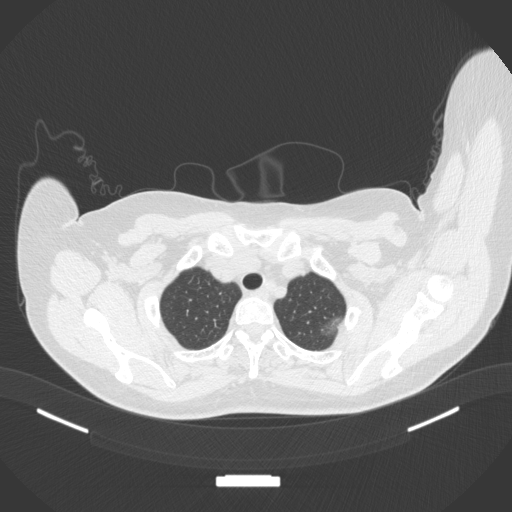
Chest CT, one axial slice; position 325 of 386 along the scan axis; reconstruction kernel B31f; lung window (W 1500 / L -600 HU); 1 mm slice thickness; 512 × 512 image matrix. Patient: female, 58 years. From the clinical record (not read from this slice): clinical TNM (as recorded): T1c N0 M0.
Outlined on this slice (rectangle marked by the reading radiologist):
- lung tumour (recorded histology: adenocarcinoma): bounding box (x1, y1, x2, y2) in pixels: (321, 311, 345, 336)